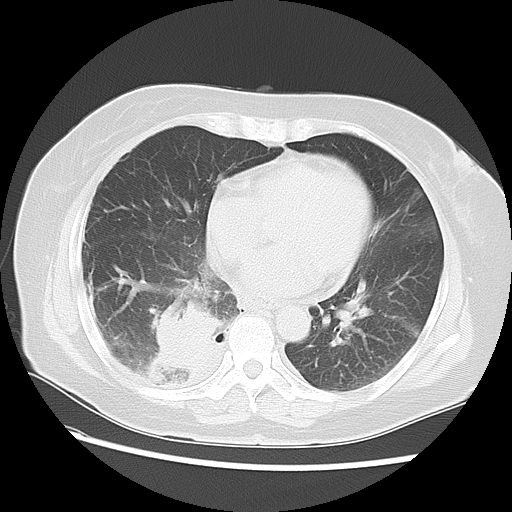
Chest CT, one axial slice. Slice 26 of 57 in the series (ordered by position). Reconstruction kernel LUNG. Lung window (W 1500 / L -600 HU). 5 mm slice thickness. 512 × 512 image matrix. Female patient, age 69 years. Case-level facts recorded for this patient, not image findings: clinical TNM (as recorded): T2 N1 M1a.
Structures marked on this image (rectangle marked by the reading radiologist):
- lung tumour (recorded histology: adenocarcinoma): bounding box [x1, y1, x2, y2] px = [137, 300, 229, 389]